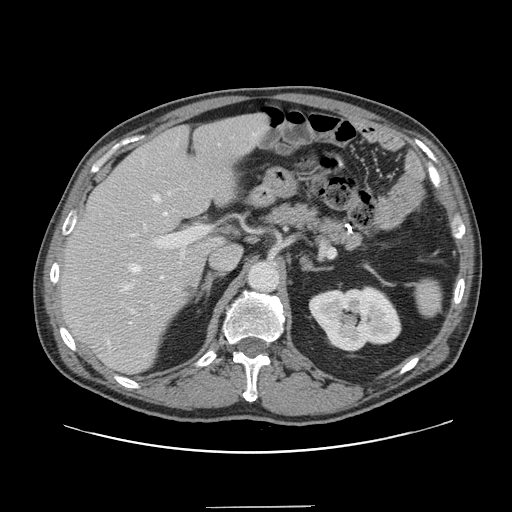
Contrast-enhanced abdominal CT, one axial slice. Position 91 of 139 along the scan axis. 120 kVp. Intravenous contrast given. Soft-tissue window (W 400 / L 40 HU). 2.5 mm slice thickness. 512 × 512 image matrix, field of view 397 × 397 mm. Male patient, age 64 years. From the clinical record (not read from this slice): diagnosis: colorectal cancer liver metastases, imaged before liver resection; multiple liver metastases: yes.
Structures marked on this image (expert manual segmentation):
- hepatic veins: bounding box <123,134,256,324> (left, top, right, bottom; pixels)
- liver: <62,115,267,373>
- planned liver remnant (the part of the liver to remain after resection): <62,115,268,372>
- portal vein (with intrahepatic branches): <122,226,210,313>
- liver metastasis: <185,287,193,296>